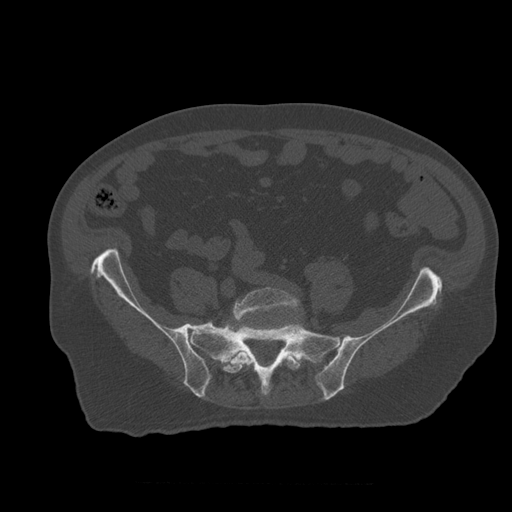
CT including the spine, one axial slice. 120 kVp. Bone window (W 1800 / L 400 HU). 1.25 mm slice thickness. 512 × 512 image matrix, field of view 407 × 407 mm. Patient age 73 years. Case-level facts recorded for this patient, not image findings: primary cancer: prostate; vertebrae with lytic lesions (as recorded): L2.
Annotated regions visible in this slice (semi-automatically segmented with operator editing):
- L5 vertebra: bounding box (x1, y1, x2, y2) in pixels: (223, 288, 301, 374)